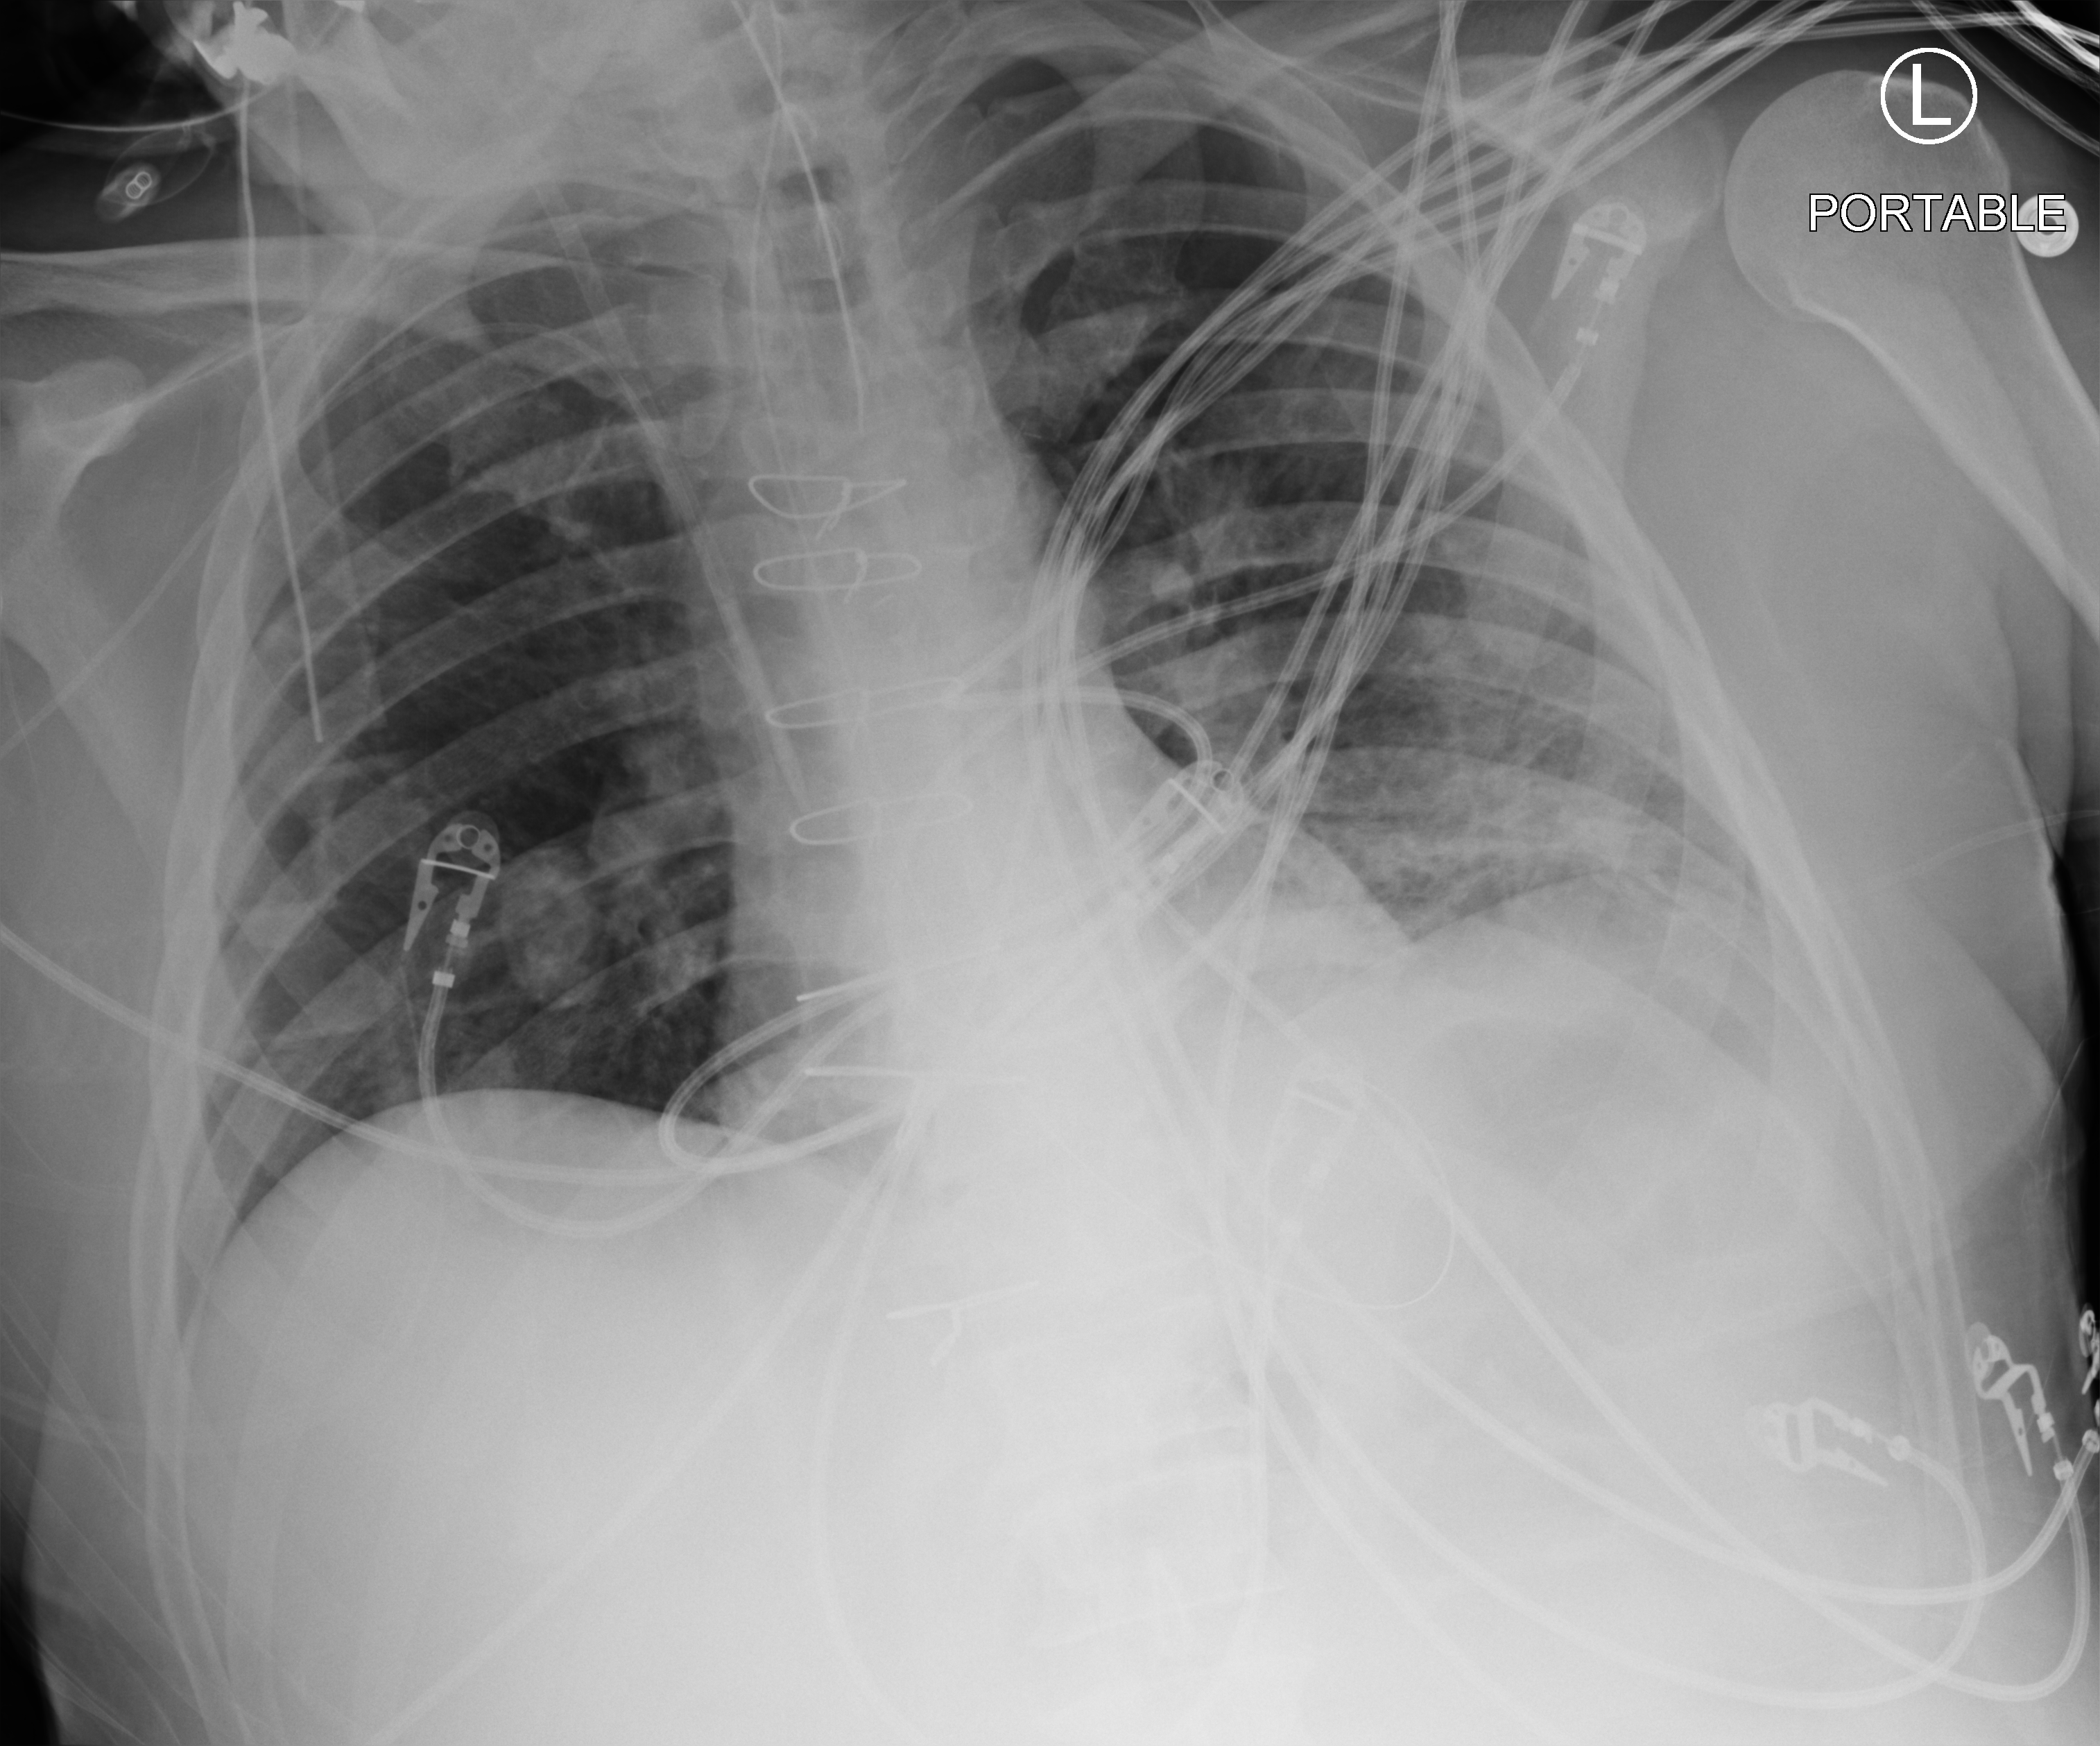
Portable chest radiograph; anteroposterior (AP) projection. Male patient hospitalised with COVID-19, age 60–74 years.
Admission-level facts for this patient (not findings on this image; timing relative to this image not recorded):
- COPD (admission record): no
- admitted to intensive care during this hospital stay: yes